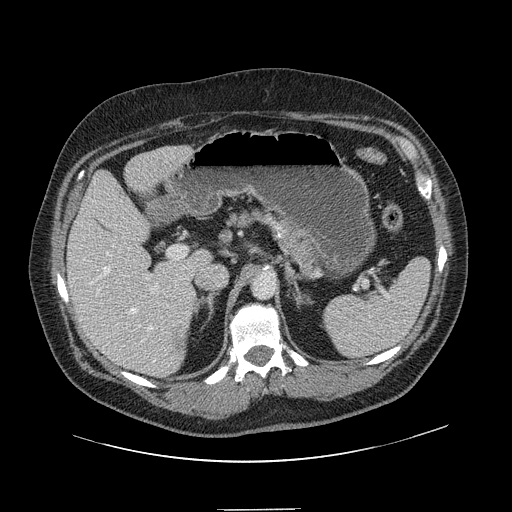
Contrast-enhanced abdominal CT, one axial slice; position 85 of 154 along the scan axis; soft-tissue window (W 400 / L 40 HU); 2.5 mm slice thickness; 512 × 512 image matrix, field of view 451 × 451 mm. Male patient, age 61 years. Case-level facts recorded for this patient, not image findings: diagnosis: colorectal cancer liver metastases, imaged before liver resection; multiple liver metastases: yes; largest metastasis: 2.6 cm; disease in both lobes: yes.
Outlined on this slice (manually delineated by an expert):
- hepatic veins: bounding box (x1, y1, x2, y2) in pixels: (103, 245, 156, 362)
- liver: (68, 146, 210, 377)
- planned liver remnant (the part of the liver to remain after resection): (69, 148, 210, 366)
- portal vein (with intrahepatic branches): (96, 253, 159, 295)
- liver metastasis: (176, 336, 187, 354)